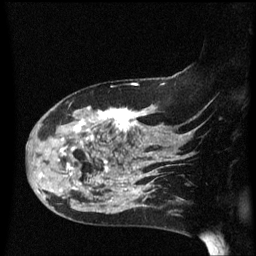
Breast MRI (dynamic contrast-enhanced), one sagittal slice. Position 42 of 60 along the scan axis. Dynamic contrast-enhanced series, image 2 of 3 at this slice position (ordered by acquisition). 1.5 T. TE 4.2 ms, TR 8.4 ms. 256 × 256 image matrix, field of view 200 × 200 mm. Patient: female, 47 years.
Annotated regions visible in this slice (semi-automatically segmented with operator editing):
- analysis volume of interest (the breast-tissue region the enhancement analysis was run in; not a lesion): bounding box [x1, y1, x2, y2] px = [28, 97, 149, 206]
- tumour enhancement mask (voxels above the 70 % enhancement threshold inside the analysis volume of interest): [60, 108, 147, 194]